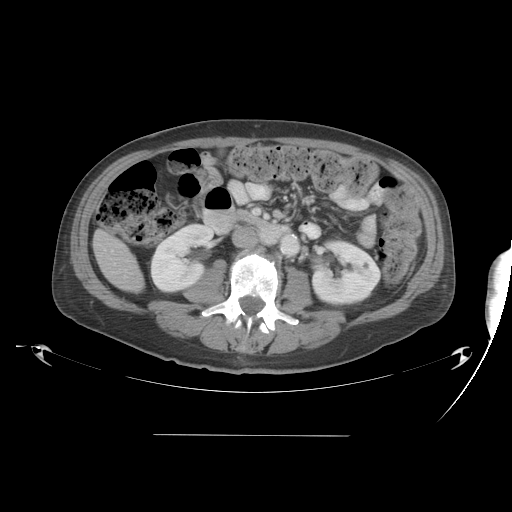
Contrast-enhanced abdominal CT, one axial slice; slice 12 of 48 in the series (ordered by position); reconstruction kernel STANDARD; 120 kVp; soft-tissue window (W 400 / L 40 HU); 5 mm slice thickness; 512 × 512 image matrix, field of view 486 × 486 mm. Male patient, age 65 years. Case-level facts recorded for this patient, not image findings: diagnosis: colorectal cancer liver metastases, imaged before liver resection; multiple liver metastases: yes; largest metastasis: 11 cm; disease in both lobes: yes.
Annotated regions visible in this slice (outlined manually by an expert reader):
- liver: box from (x=95, y=232) to (x=143, y=292) px